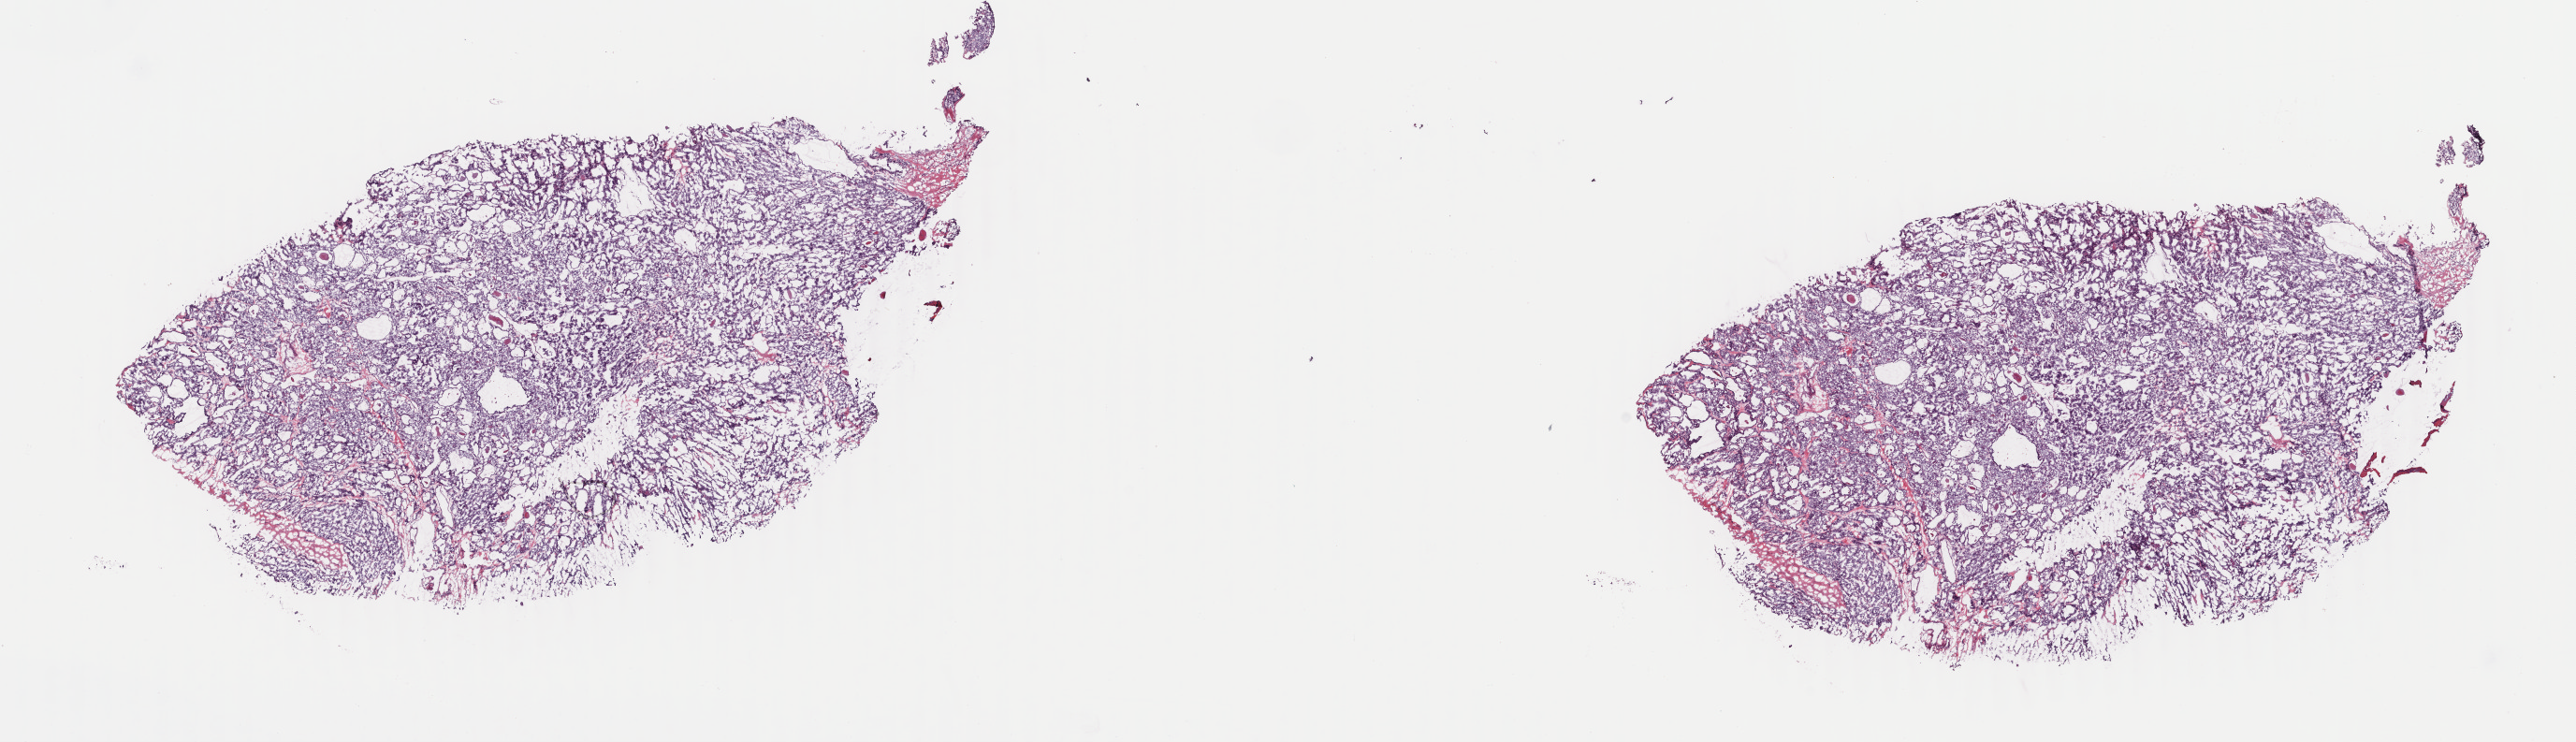
Digitized H&E-stained tissue section (whole slide), whole scanned area (about 21.9 x 6.3 mm, from a 40x scan) shown as a low-resolution overview, frozen section from the top of the tissue portion, sample: primary tumour, thyroid. Male, age 35 years at initial diagnosis.
Pathologic diagnosis: Papillary carcinoma, follicular variant.